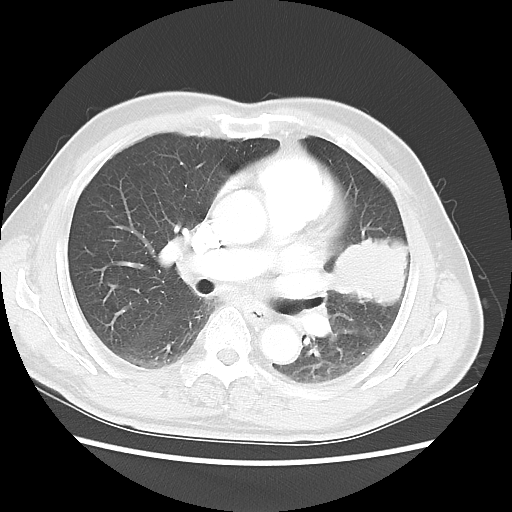
Chest CT, one axial slice. Position 28 of 50 along the scan axis. Reconstruction kernel LUNG. Lung window (W 1500 / L -600 HU). 512 × 512 image matrix, field of view 360 × 360 mm. Male patient, age 69 years. From the clinical record (not read from this slice): clinical TNM (as recorded): T3 N1 M1a.
Outlined on this slice (rectangle marked by the reading radiologist):
- lung tumour (recorded histology: squamous cell carcinoma): box from (x=331, y=231) to (x=427, y=312) px